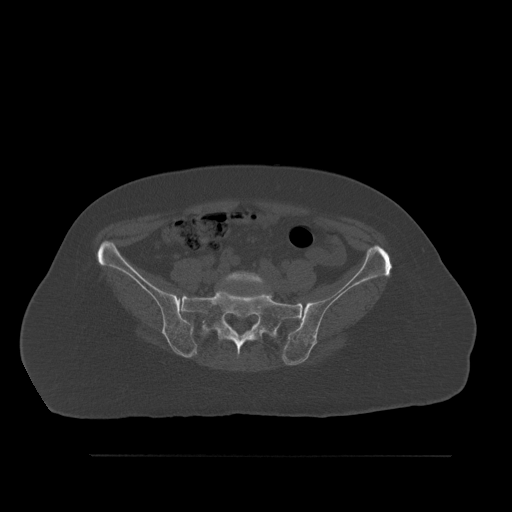
CT including the spine, one axial slice. Slice 174 of 527 in the series (ordered by position). Bone window (W 1800 / L 400 HU). 512 × 512 image matrix, field of view 470 × 470 mm. Patient: female, 73 years. Case-level facts recorded for this patient, not image findings: primary cancer: breast; vertebrae with lytic lesions (as recorded): L2.
Structures marked on this image (semi-automatic segmentation, software-assisted and operator-edited):
- L5 vertebra: bounding box [x1, y1, x2, y2] px = [223, 271, 270, 290]